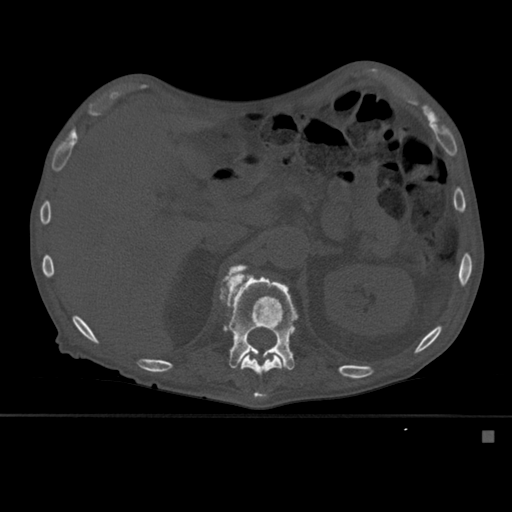
CT including the spine, one axial slice. Position 264 of 527 along the scan axis. Bone window (W 1800 / L 400 HU). 1.5 mm slice thickness. 512 × 512 image matrix, field of view 373 × 373 mm. Patient: male, 78 years. Case-level facts recorded for this patient, not image findings: primary cancer: prostate.
Annotated regions visible in this slice (semi-automatic segmentation, software-assisted and operator-edited):
- L1 vertebra: bounding box [x1, y1, x2, y2] px = [219, 273, 300, 399]
- T12 vertebra: [228, 264, 282, 398]